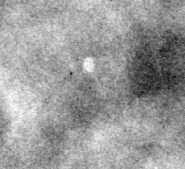
Crop from a digitized film mammogram around one marked abnormality; right breast; MLO view.
Calcifications, morphology lucent center; BI-RADS assessment category 2; subtlety rating 4 on a 1 (subtle) to 5 (obvious) scale; benign without callback (not worked up further).